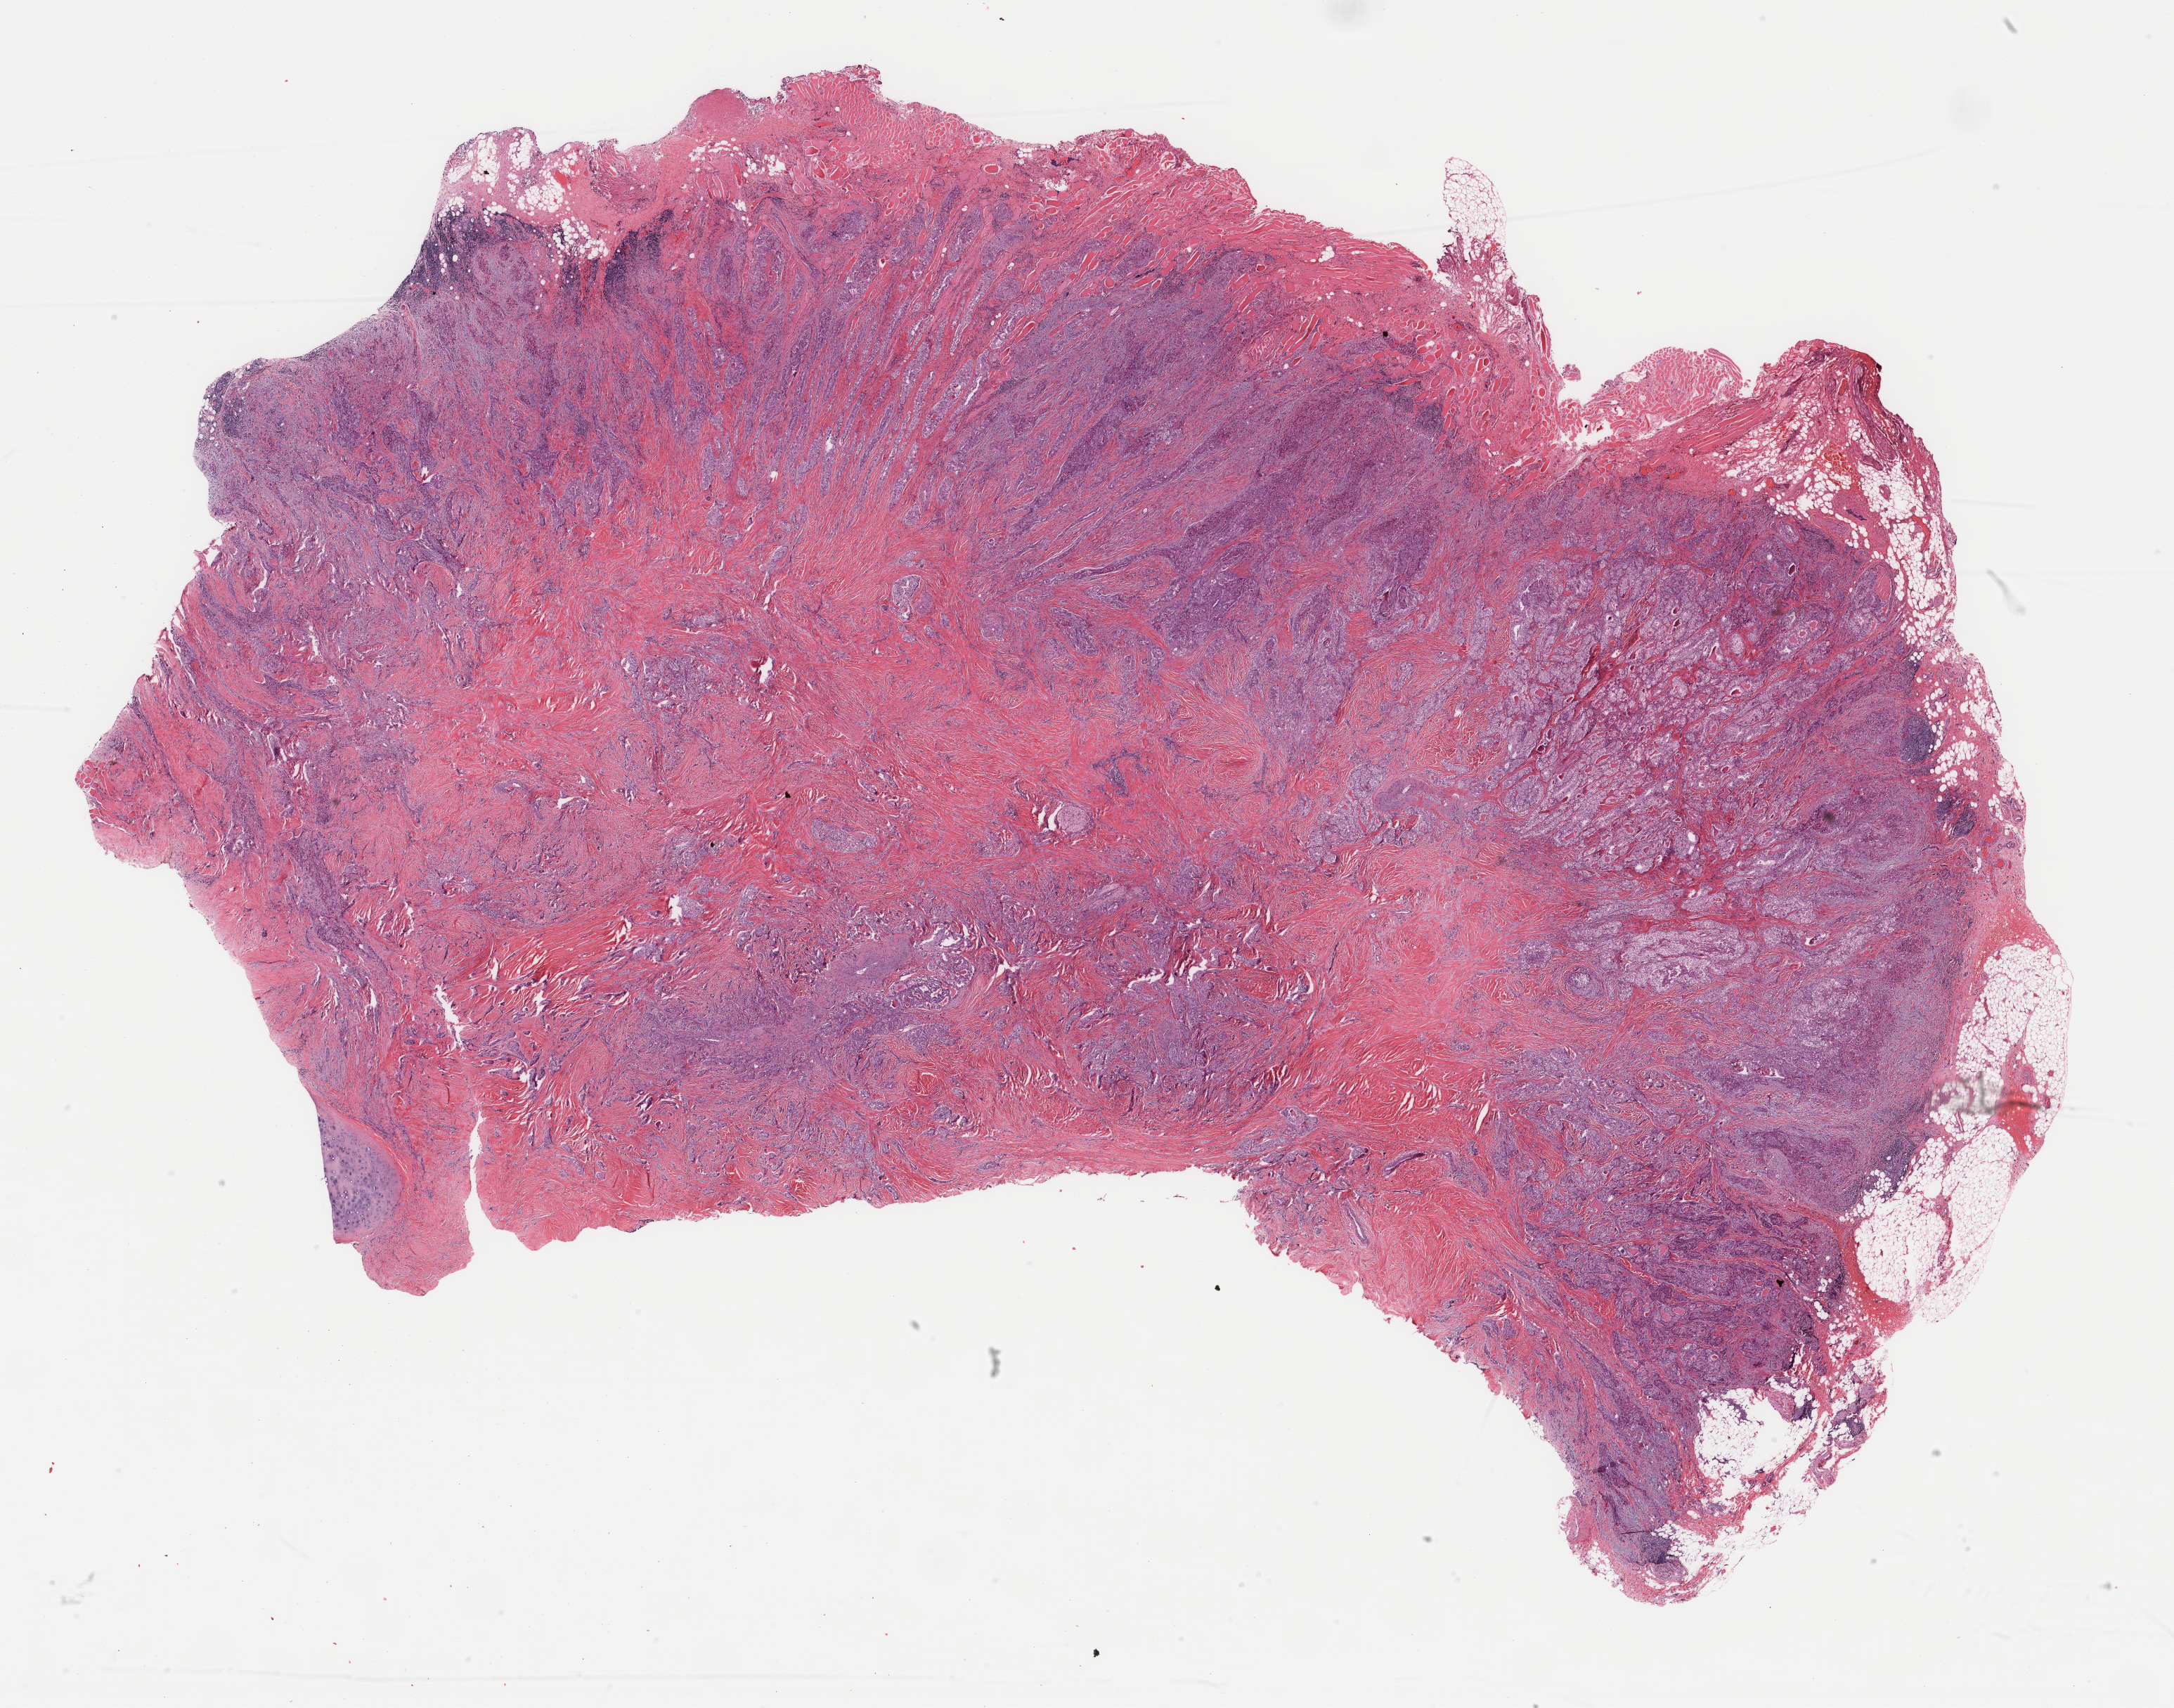
H&E whole-slide image — a low-resolution overview of the entire scanned area, about 24.6 x 19.3 mm (from a 40x scan). Formalin-fixed paraffin-embedded (FFPE) diagnostic section. Sample: primary tumour, thyroid. Female, age 57 years at initial diagnosis.
- histologic diagnosis: Papillary adenocarcinoma, NOS (thyroid gland)
- AJCC pathologic stage: IVA (6th edition)